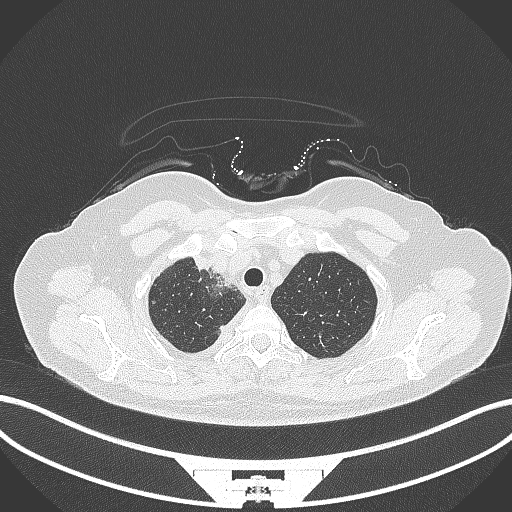
Chest CT, one axial slice. Slice 266 of 305 in the series (ordered by position). Reconstruction kernel B70f. Lung window (W 1500 / L -600 HU). 1 mm slice thickness. 512 × 512 image matrix, field of view 400 × 400 mm. Female patient, age 52 years. Case-level facts recorded for this patient, not image findings: clinical TNM (as recorded): T3 N1 M1.
Structures marked on this image (rectangle marked by the reading radiologist):
- lung tumour (recorded histology: adenocarcinoma): bounding box [x1, y1, x2, y2] px = [192, 251, 215, 275]